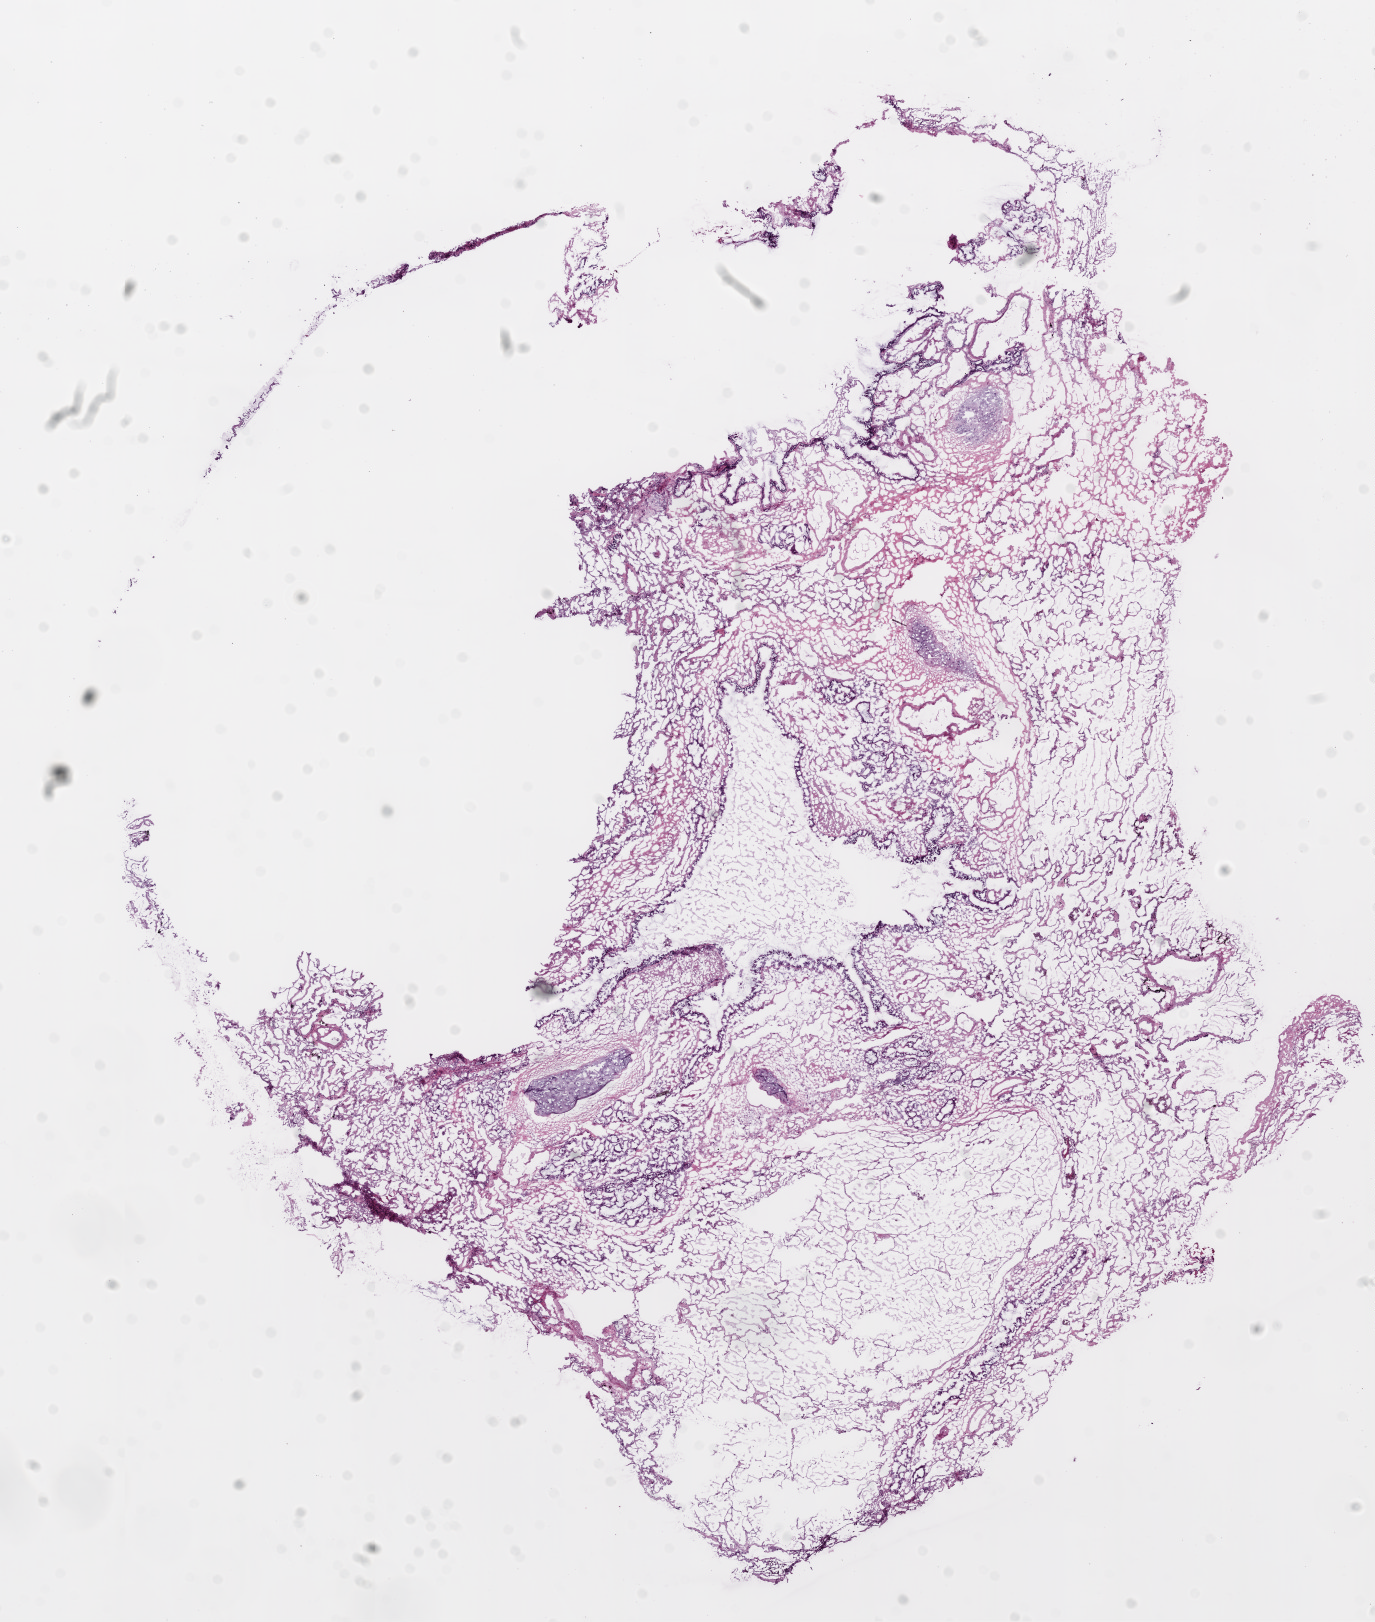
Whole-slide histology image, H&E, shown as a low-resolution overview of the whole scanned area (about 11.0 x 13.0 mm, from a 20x scan). Frozen section from the bottom of the tissue portion. Solid tissue normal (non-tumour tissue) sample from the lung. Patient: female, age at initial diagnosis 72 years.
This section: solid tissue normal (non-tumour) sample from the same patient. Patient diagnosis: Adenocarcinoma, NOS (upper lobe, lung).